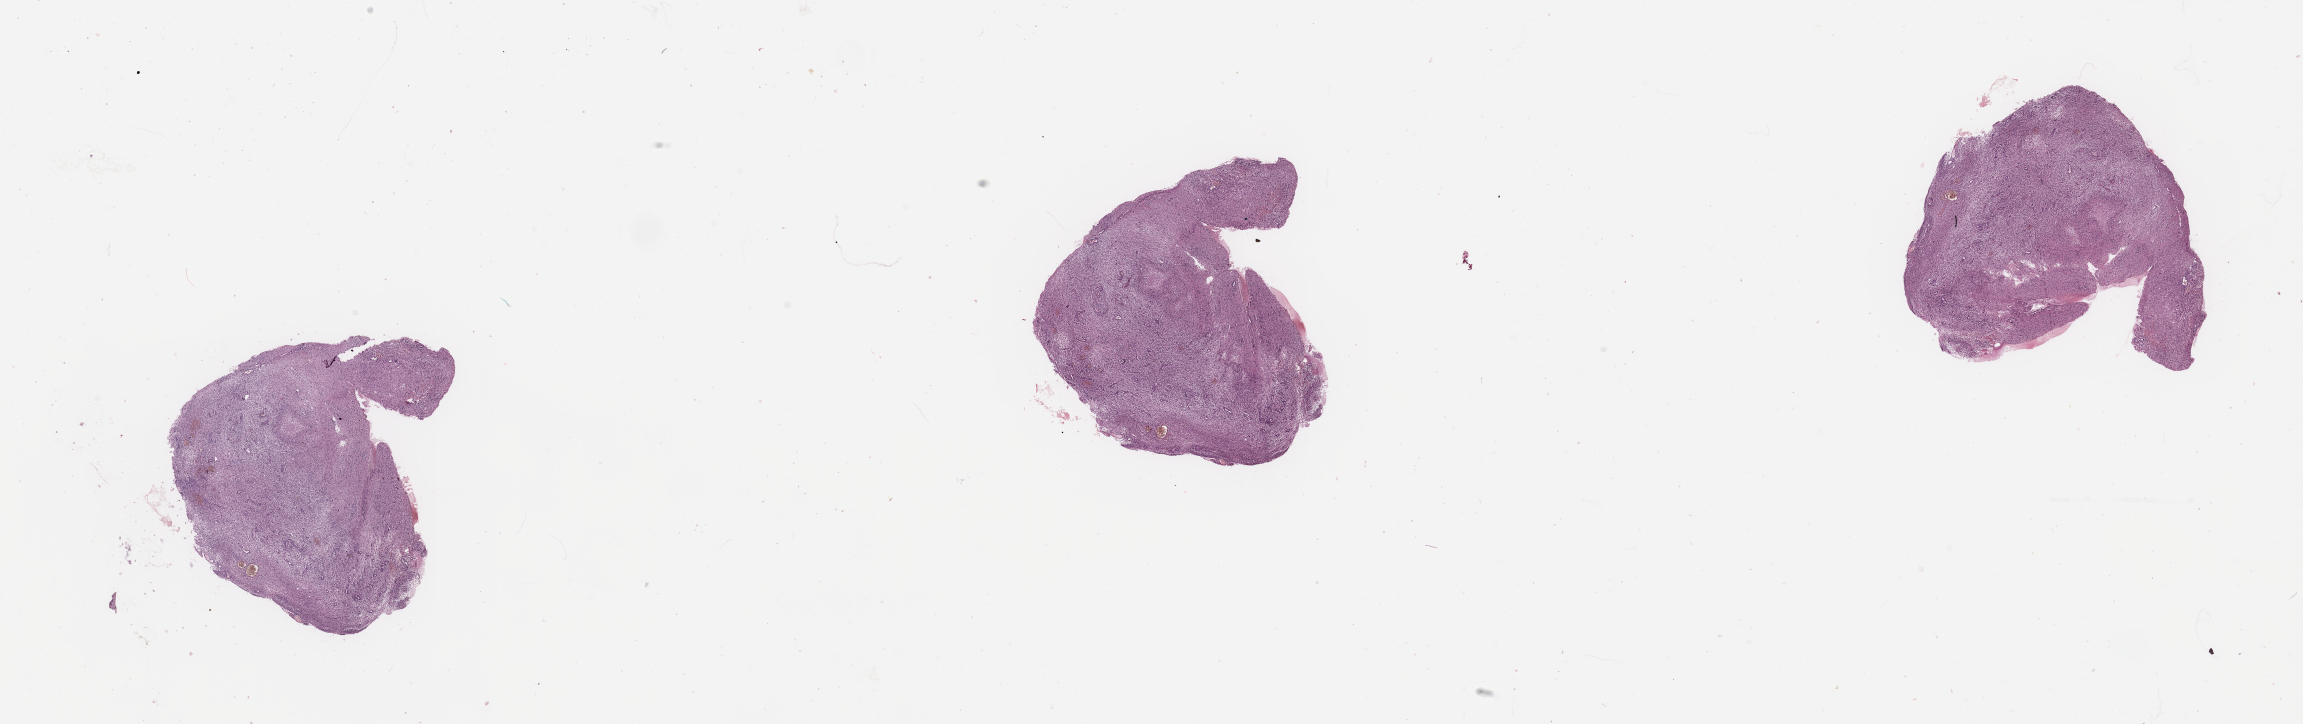
Whole-slide histology image, Hematoxylin and eosin (H&E) stained — a low-resolution overview of the entire scanned area, about 36.4 x 11.5 mm, brain, tumour tissue. Patient: female, age 58 years.
Diagnosis: Glioblastoma.